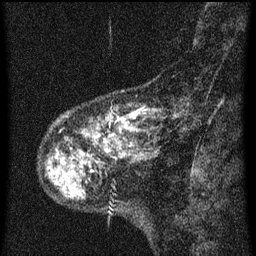
Breast MRI (dynamic contrast-enhanced), one sagittal slice; position 11 of 60 along the scan axis; dynamic contrast-enhanced series, image 2 of 3 at this slice position (ordered by acquisition); 1.5 T; TE 4.2 ms, TR 8 ms; 2 mm slice thickness; 256 × 256 image matrix. Female patient, age 55 years.
Structures marked on this image (semi-automatically segmented with operator editing):
- analysis volume of interest (the breast-tissue region the enhancement analysis was run in; not a lesion): bounding box <38,92,163,159> (left, top, right, bottom; pixels)
- tumour enhancement mask (voxels above the 70 % enhancement threshold inside the analysis volume of interest): <116,110,139,123>